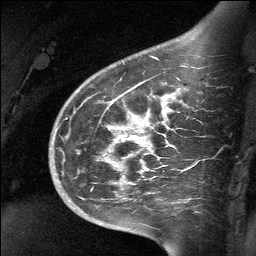
Breast MRI (dynamic contrast-enhanced), one sagittal slice; position 46 of 64 along the scan axis; dynamic contrast-enhanced study with each time point stored as its own series, time point 2 of 3 at this slice position (early post-contrast, ordered by acquisition time); 1.5 T; TE 4.8 ms, TR 27 ms; 2 mm slice thickness; 256 × 256 image matrix, field of view 200 × 200 mm. Patient: female, 39 years. From the clinical record (not read from this slice): setting: breast cancer imaged before/during neoadjuvant chemotherapy; receptor status: HER2-positive.
Outlined on this slice (semi-automatic segmentation, software-assisted and operator-edited):
- analysis volume of interest (the breast-tissue region the enhancement analysis was run in; not a lesion): box from (x=70, y=69) to (x=202, y=224) px
- tumour enhancement mask (voxels above the 90 % enhancement threshold inside the analysis volume of interest): (x=111, y=95)–(x=165, y=150)